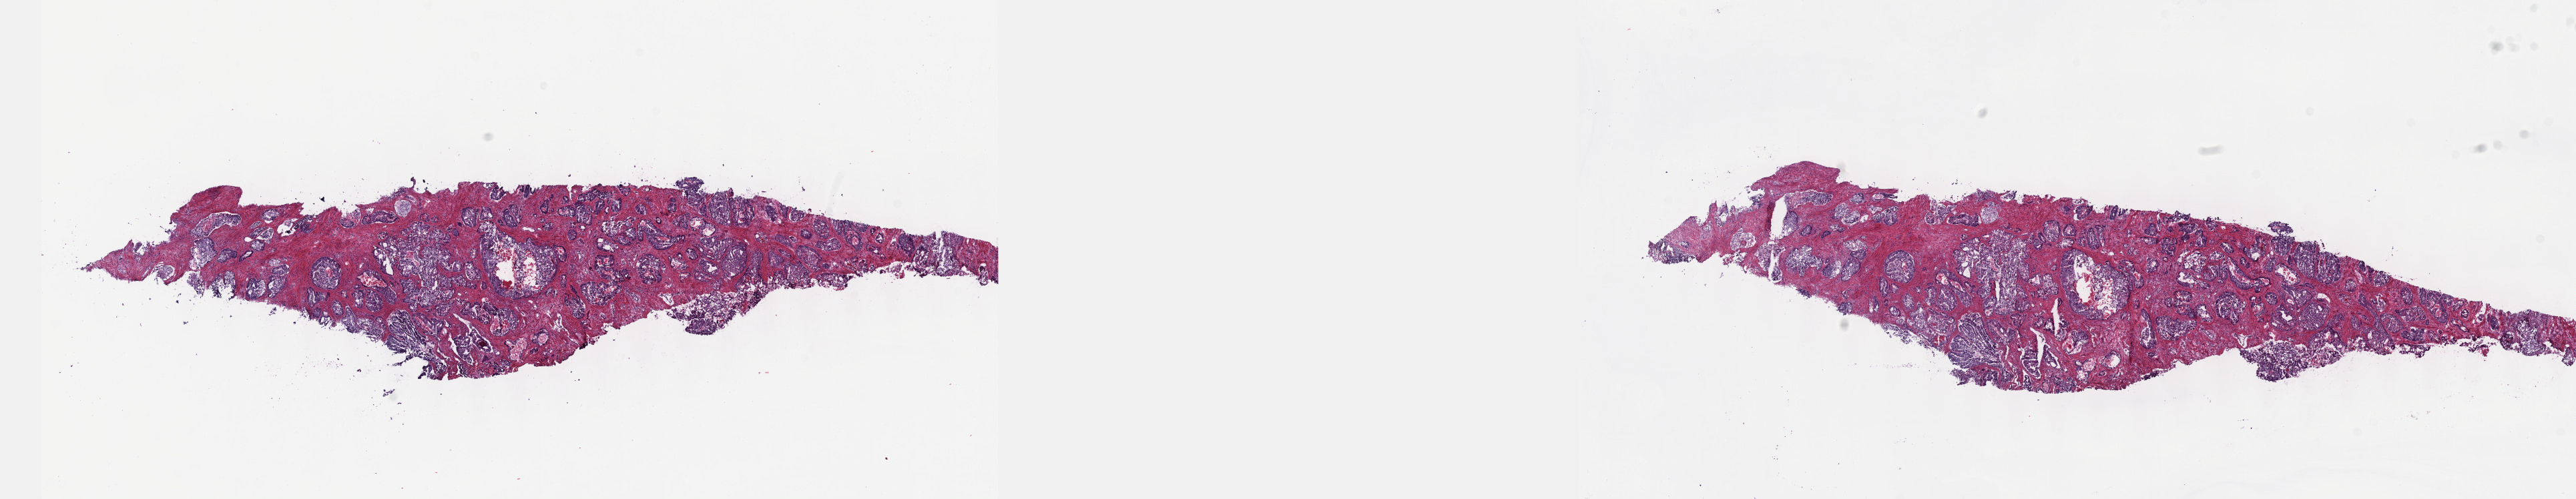
Digitized Hematoxylin and eosin (H&E) stained tissue section (whole slide), whole scanned area (about 31.2 x 6.0 mm) shown as a low-resolution overview, frozen section, prostate, primary tumour sample. Male patient; age at initial diagnosis 59 years. Gleason score: 9 (4+5). Pathologist review of this section (percent, as recorded): tumour cells 85%, tumour nuclei 70%, normal cells 0%, stromal cells 0%, necrosis 15%. Infiltration values recorded for this section: lymphocyte infiltration 0%, monocyte infiltration 0%, neutrophil infiltration 0%.
• pathologic diagnosis: Adenocarcinoma, NOS (prostate gland)